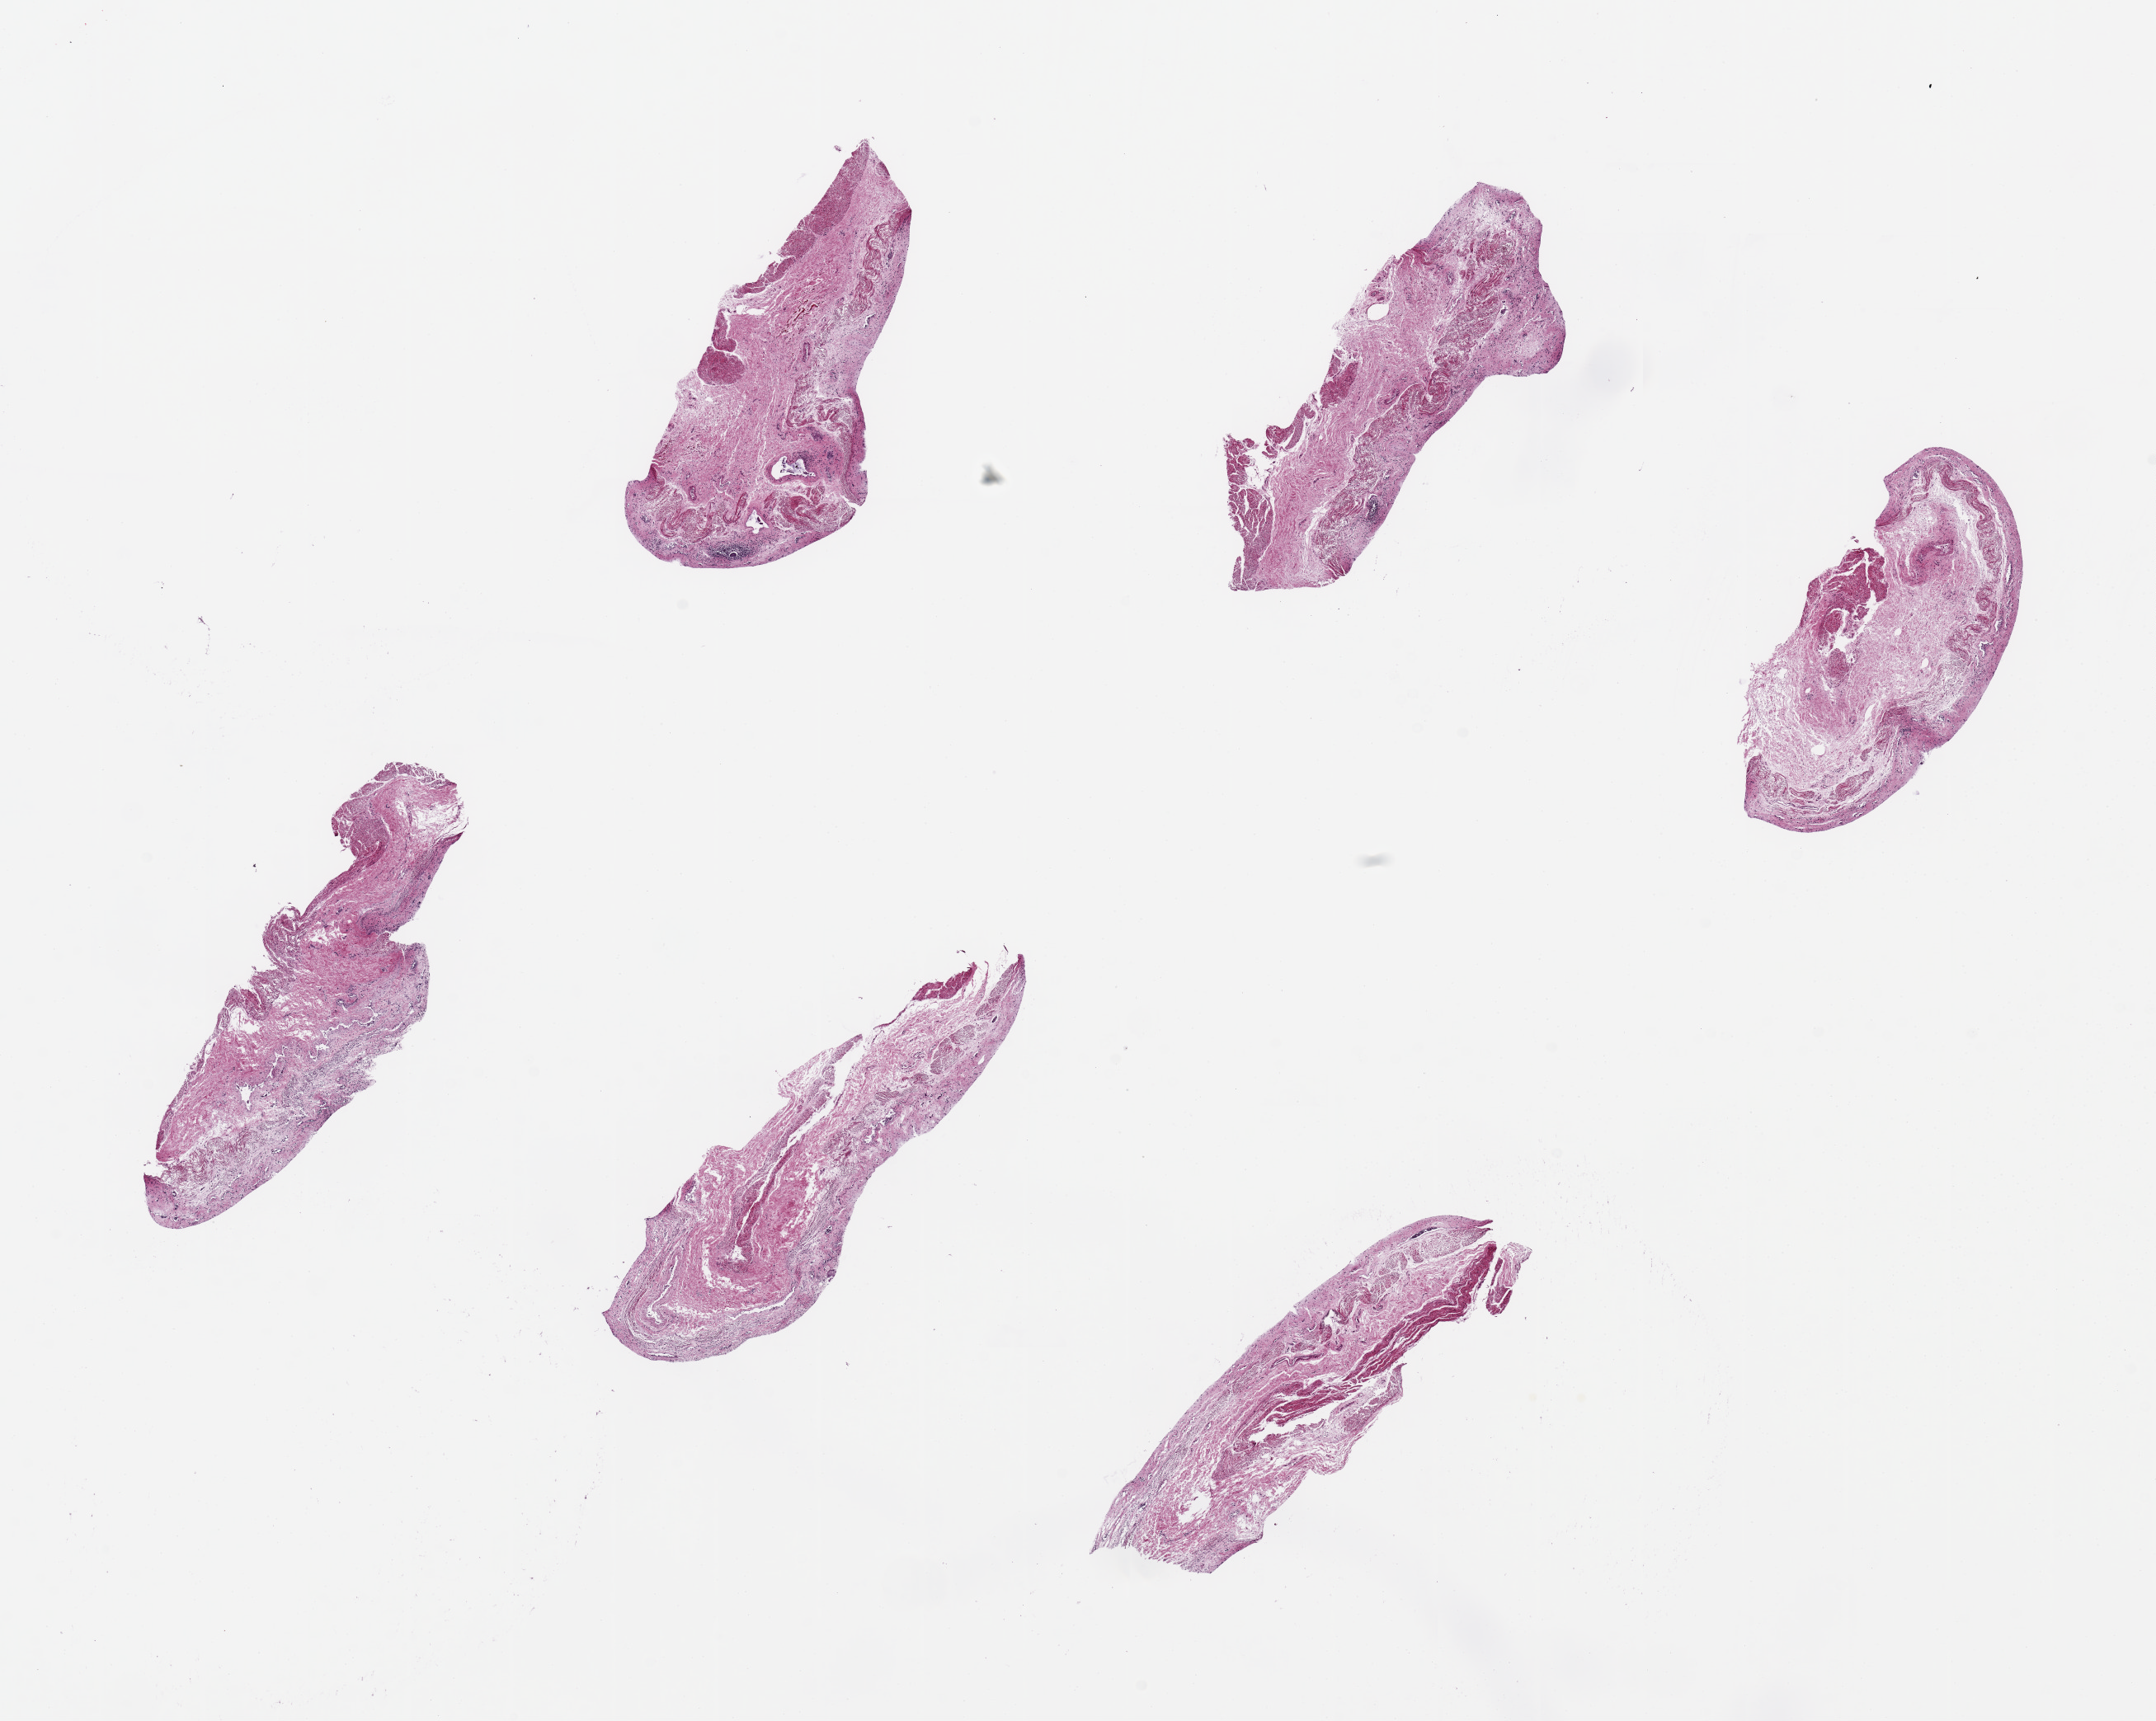
Haematoxylin and eosin whole-slide image, brightfield, a low-resolution overview of the entire scanned area, about 20.7 x 16.5 mm (from a 20x scan). PAXgene-fixed paraffin-embedded (PFPE) section. Target tissue: esophageal mucous membrane. Donor tissue sample. Donor sex: female.
Reviewer comment on this tissue sample: 6 pieces ~5x2mm. Mucosa completely sloughed.